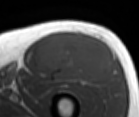
MRI of an extremity soft-tissue mass, one axial slice; position 53 of 86 along the scan axis; MR volume resampled by the dataset authors to the PET/CT grid (not the native acquisition matrix); 139 × 117 image matrix, field of view 136 × 114 mm. Male patient. Case-level facts recorded for this patient, not image findings: histological type: extraskeletal osteosarcoma; grade: high; site of the primary tumour: thigh.
Annotated regions visible in this slice (expert contour drawn on MRI and transferred to this co-registered scan by the dataset authors):
- gross tumour volume (mass): bounding box [x1, y1, x2, y2] px = [38, 32, 114, 83]